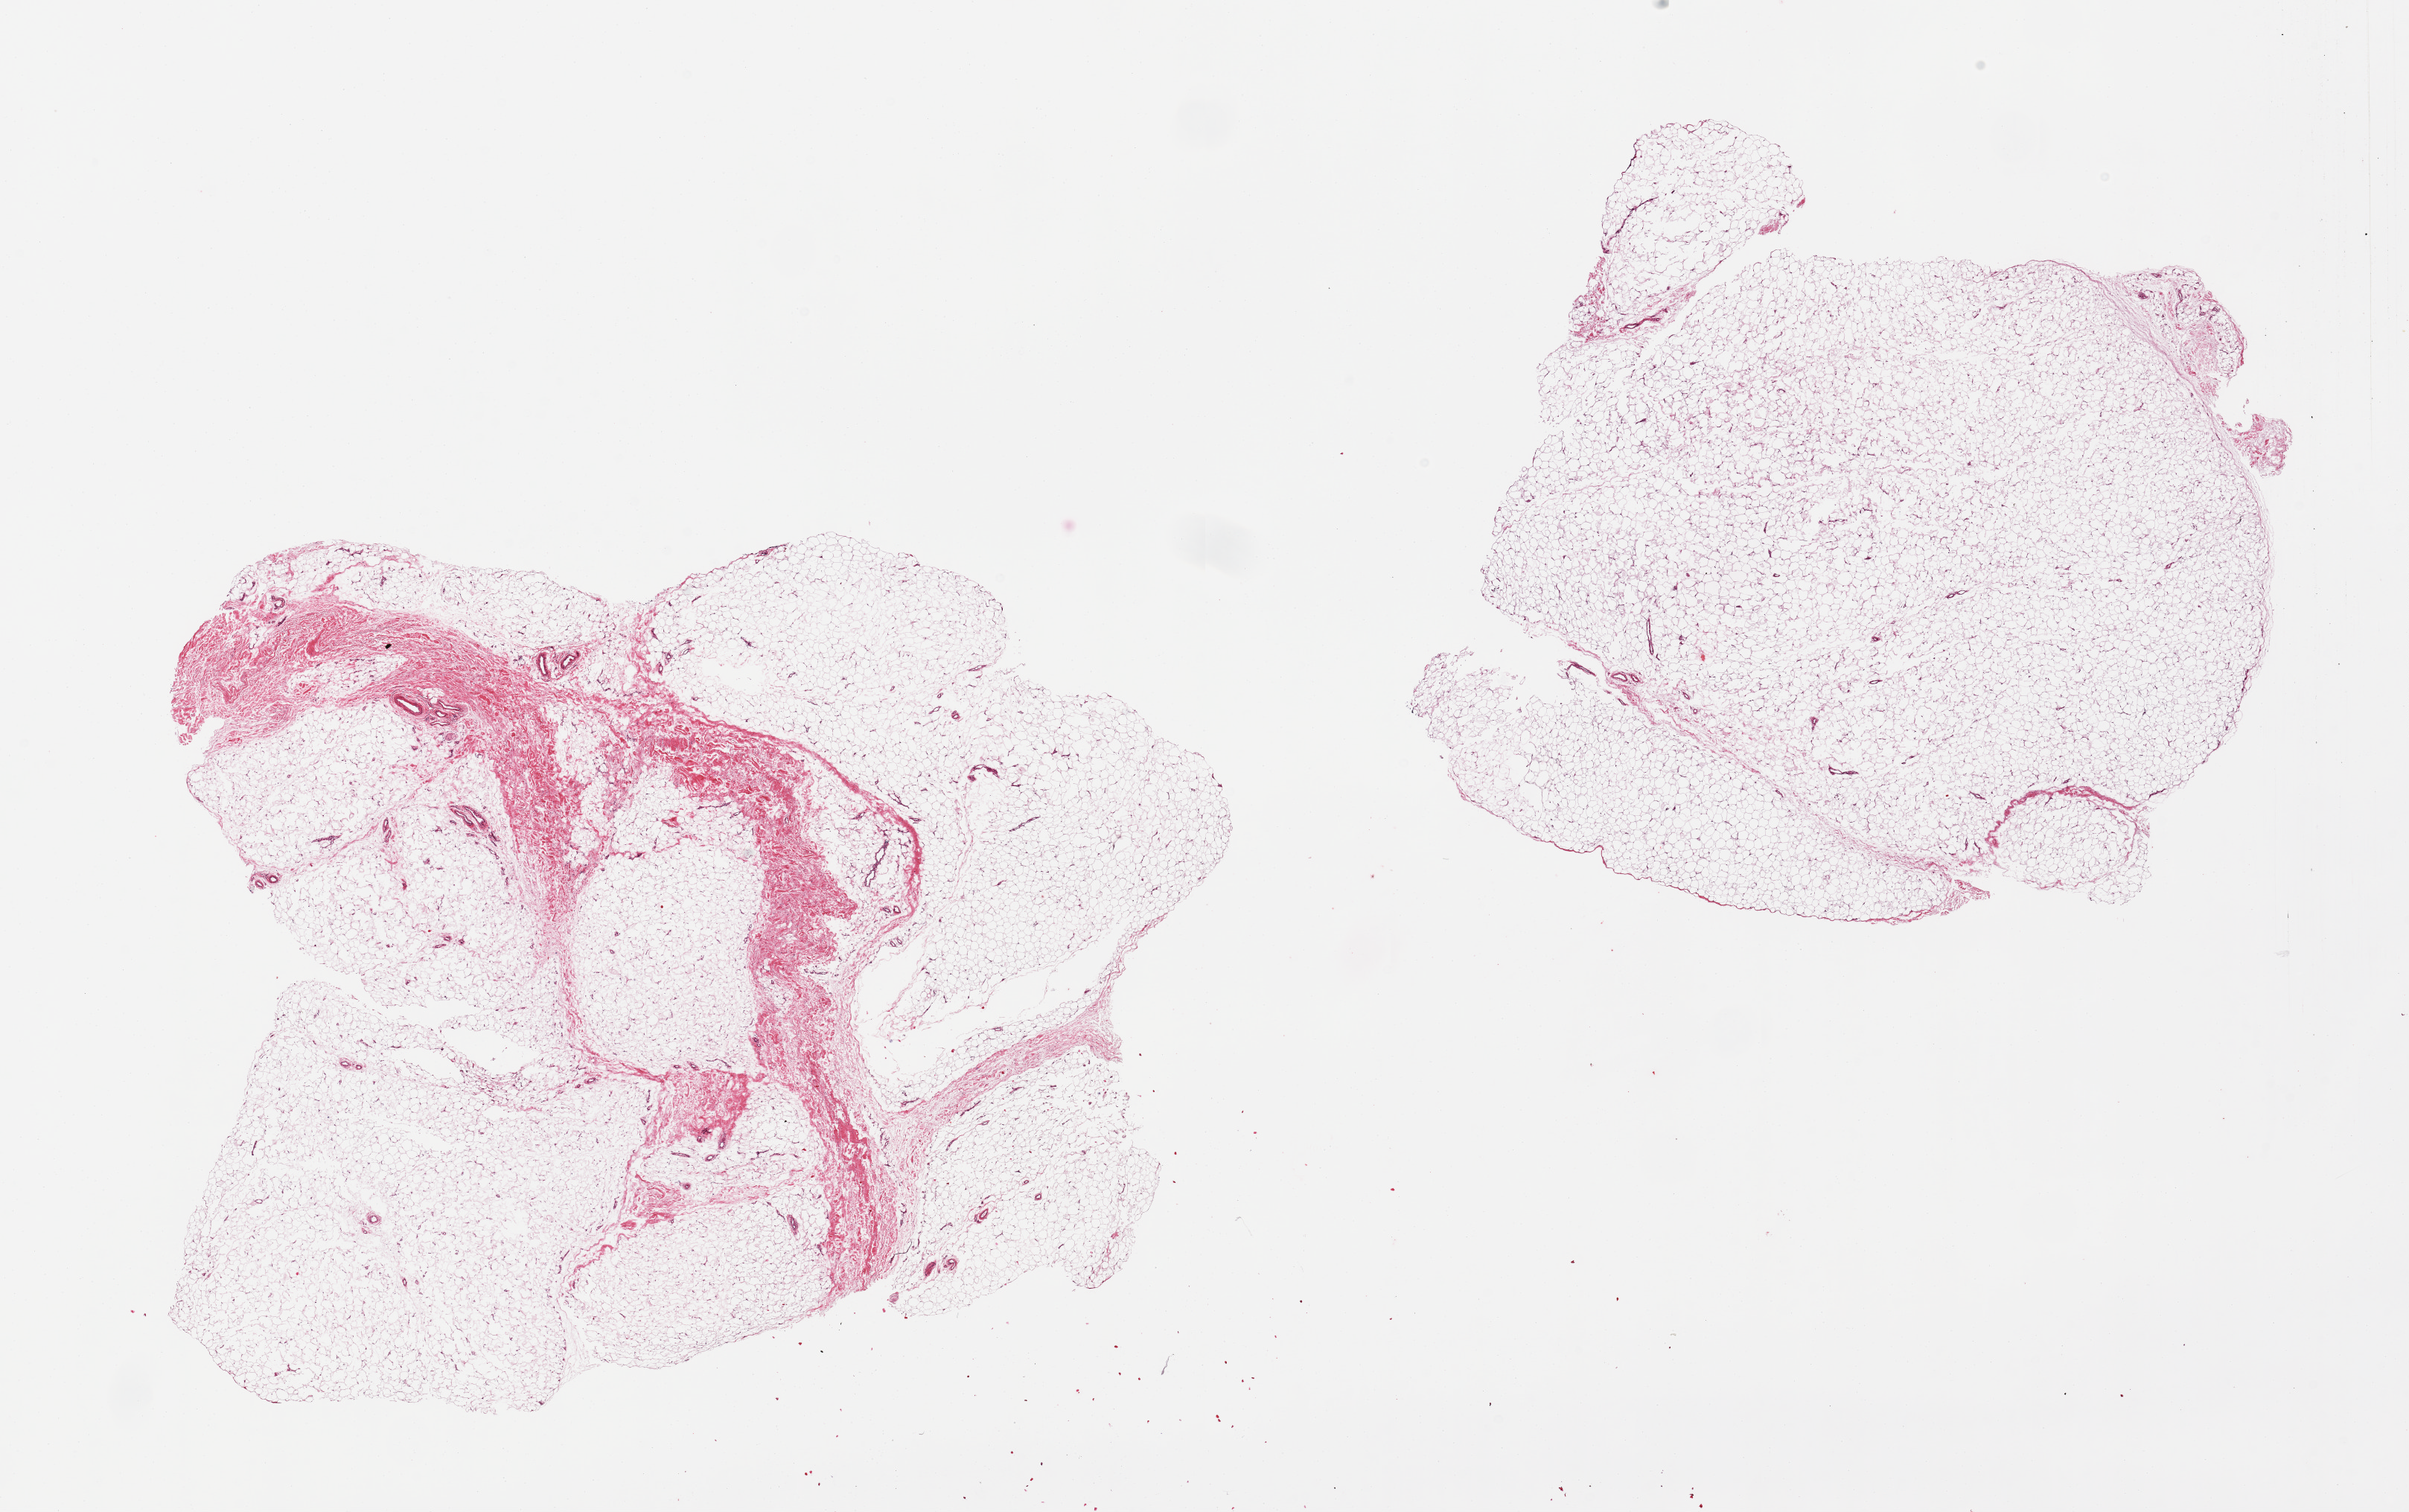
Whole-slide image, haematoxylin and eosin stain, shown as a low-resolution overview of the whole scanned area (about 25.6 x 16.1 mm, slide scanned at 20x), PAXgene-fixed paraffin-embedded (PFPE) section, target tissue: adipose tissue, tissue donor sample. Female donor.
Review note (as recorded): 2 pieces, ~10% fascia.